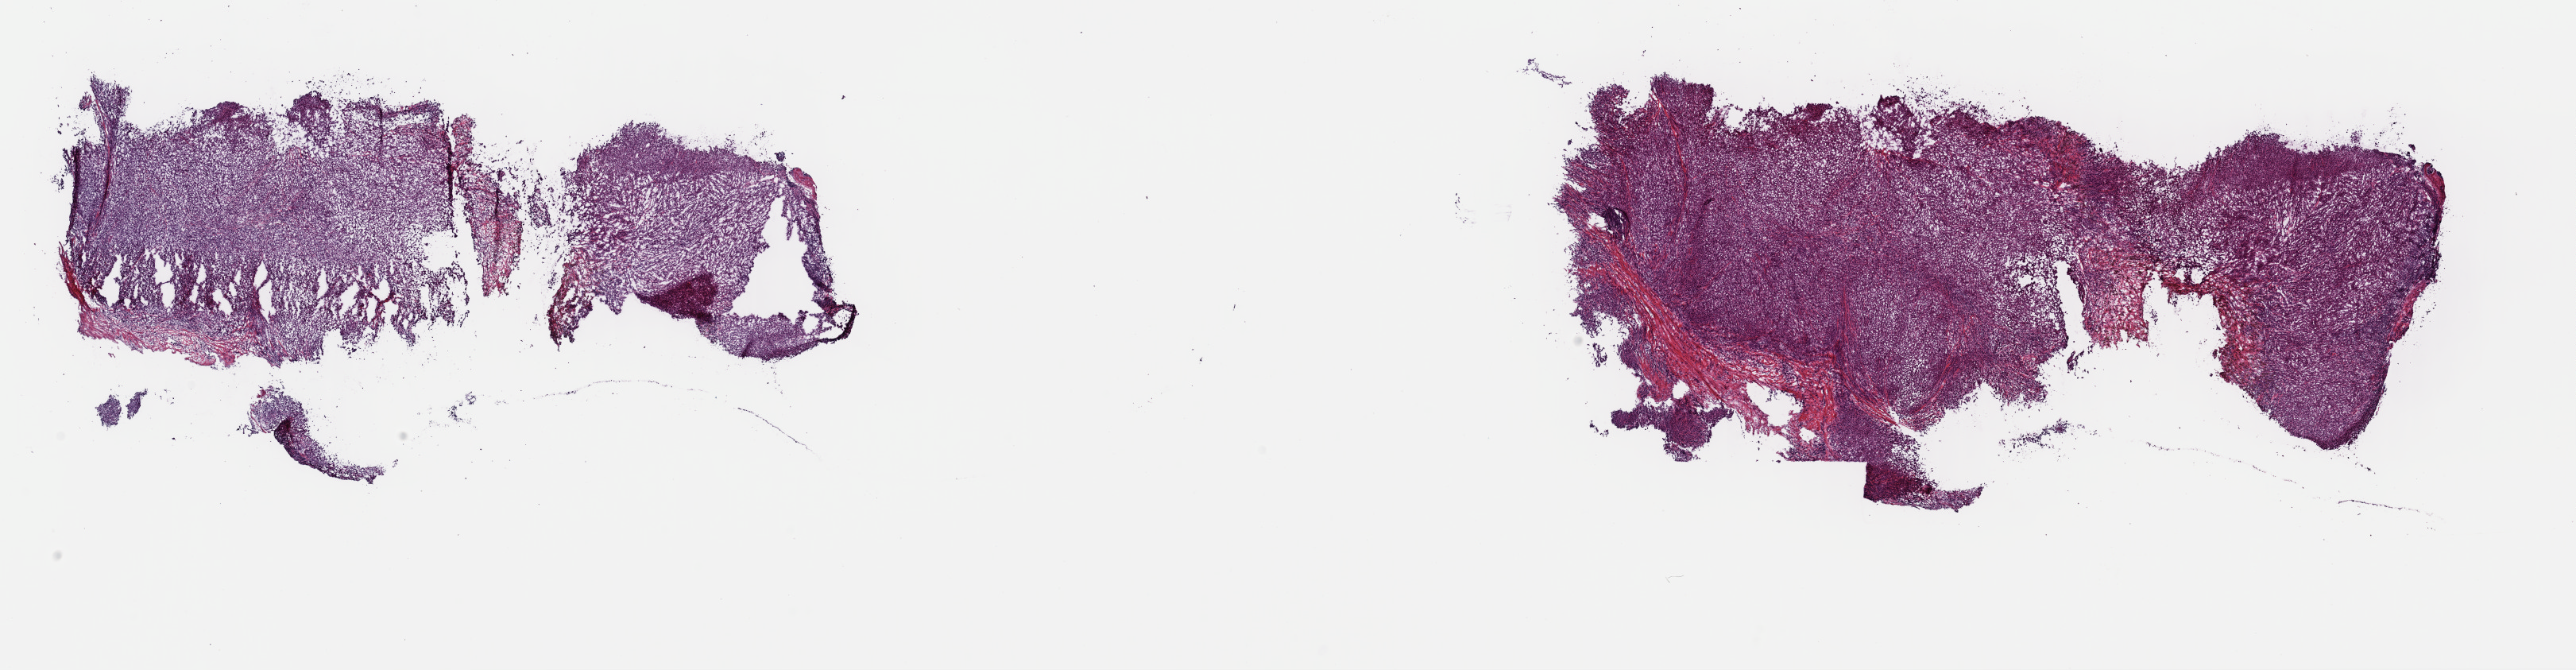
Digitized H&E tissue section (whole slide) — low-resolution overview of the scanned area, about 25.6 x 6.7 mm (from a 40x scan), frozen section from the top of the tissue portion, metastatic tumour sample. Male patient; age at initial diagnosis 44 years. Pathologist review of this section (percent, as recorded): tumour cells 75%, tumour nuclei 75%, normal cells 0%, stromal cells 25%, necrosis 0%. Inflammatory infiltration, as recorded: lymphocyte infiltration 10%, monocyte infiltration 0%, neutrophil infiltration 0%.
This section: metastatic tumour tissue. Patient diagnosis: Malignant melanoma, NOS.